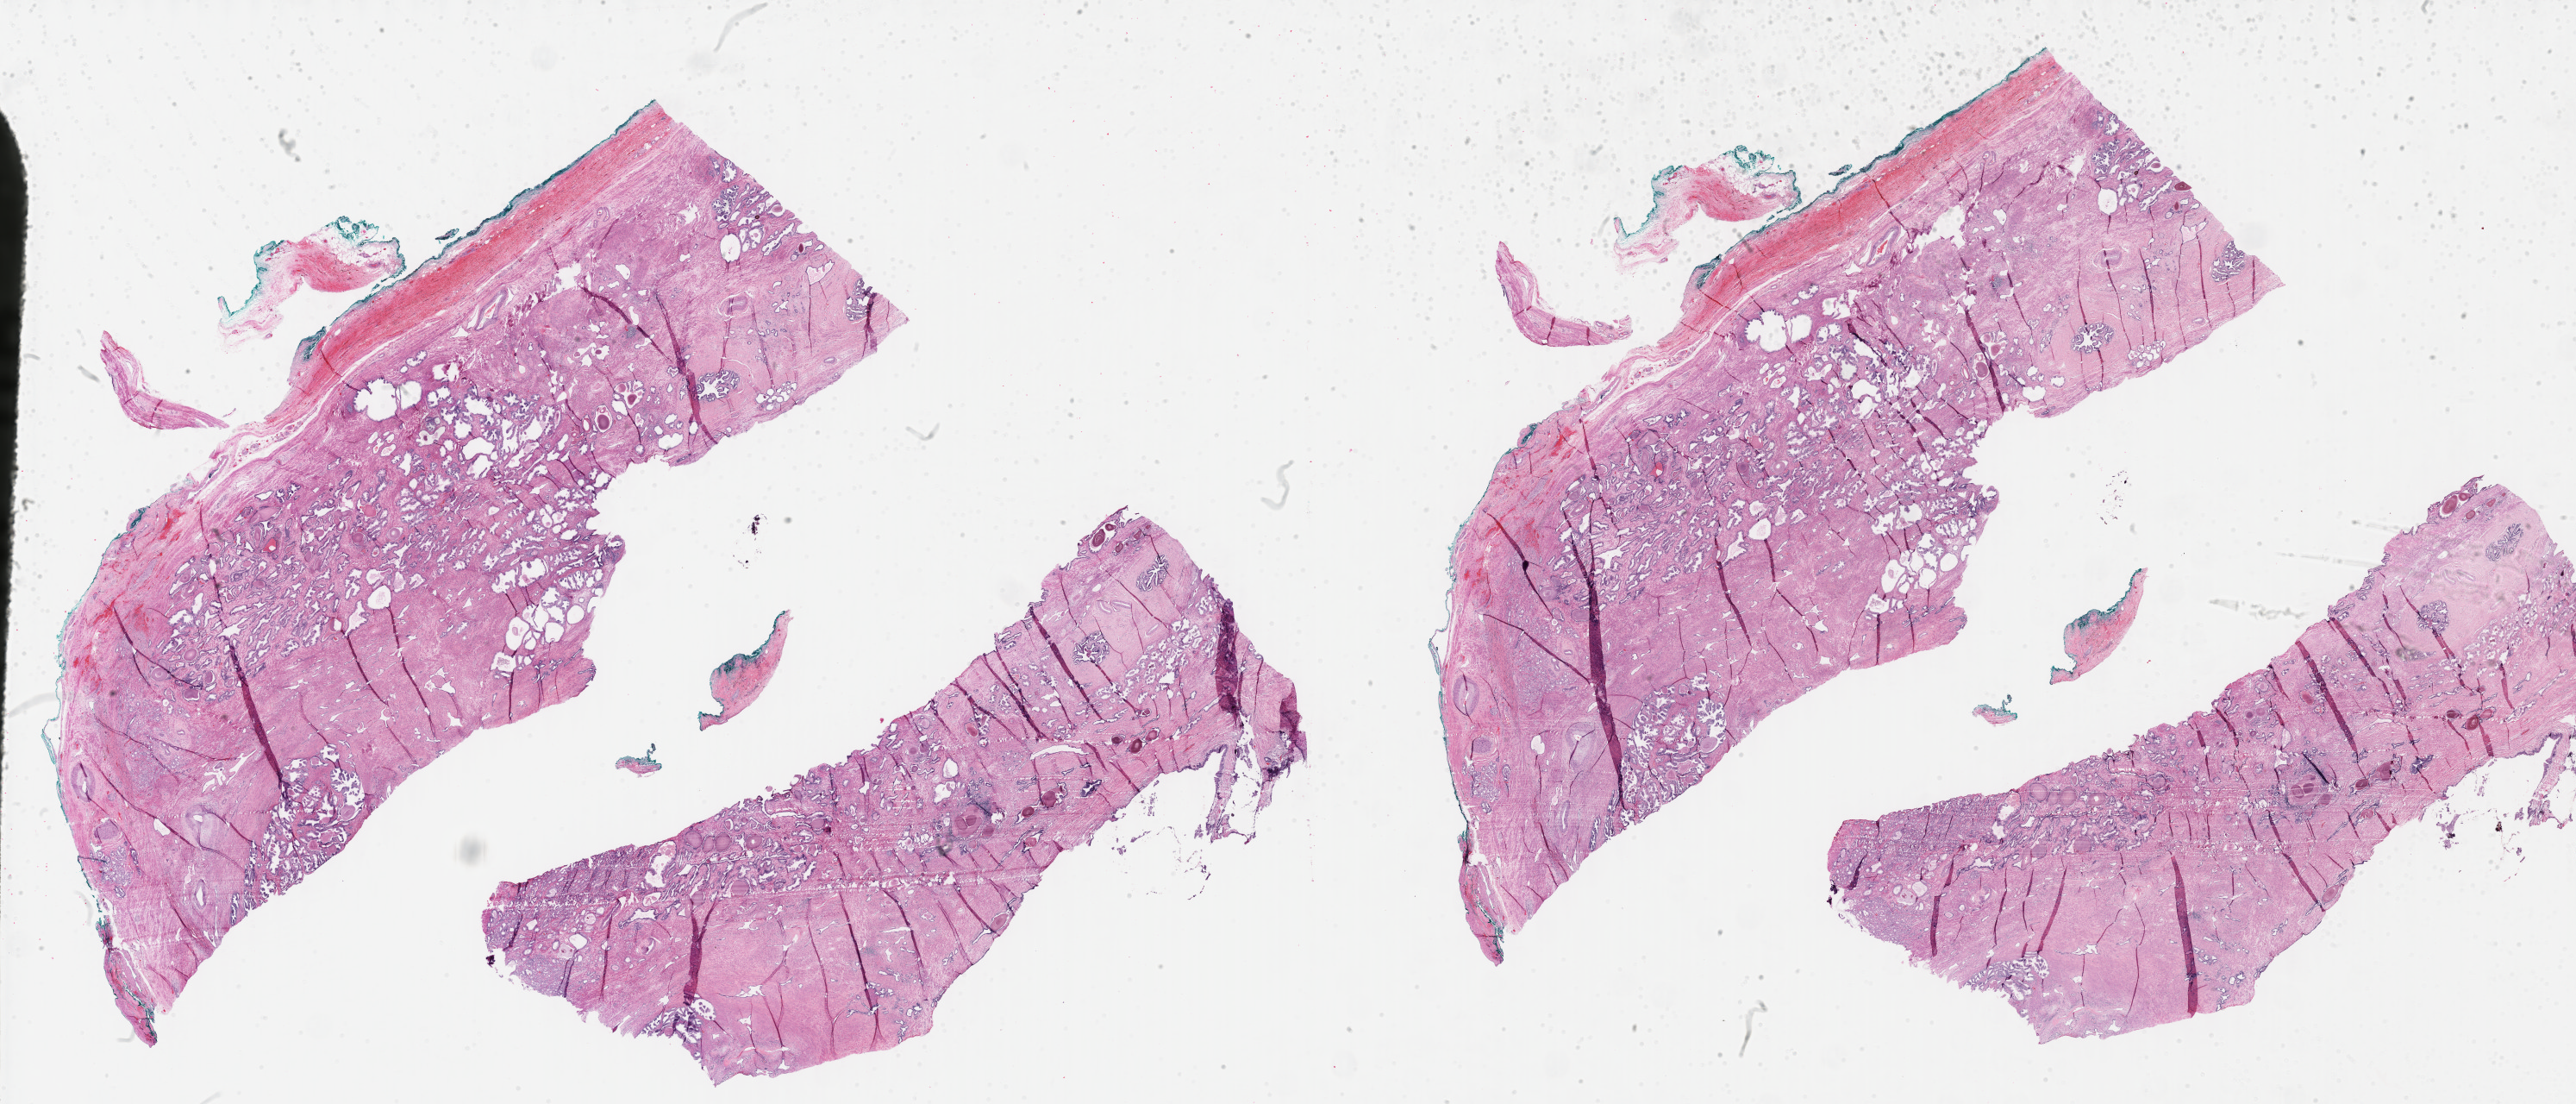
Digitized H&E-stained tissue section (whole slide) — whole scanned area (about 48.3 x 20.7 mm) shown as a low-resolution overview, formalin-fixed paraffin-embedded (FFPE) diagnostic section, sample: primary tumour, prostate. Male patient; age at initial diagnosis 64 years. Gleason score: 7 (3+4).
Histologic diagnosis: Adenocarcinoma, NOS (prostate gland).